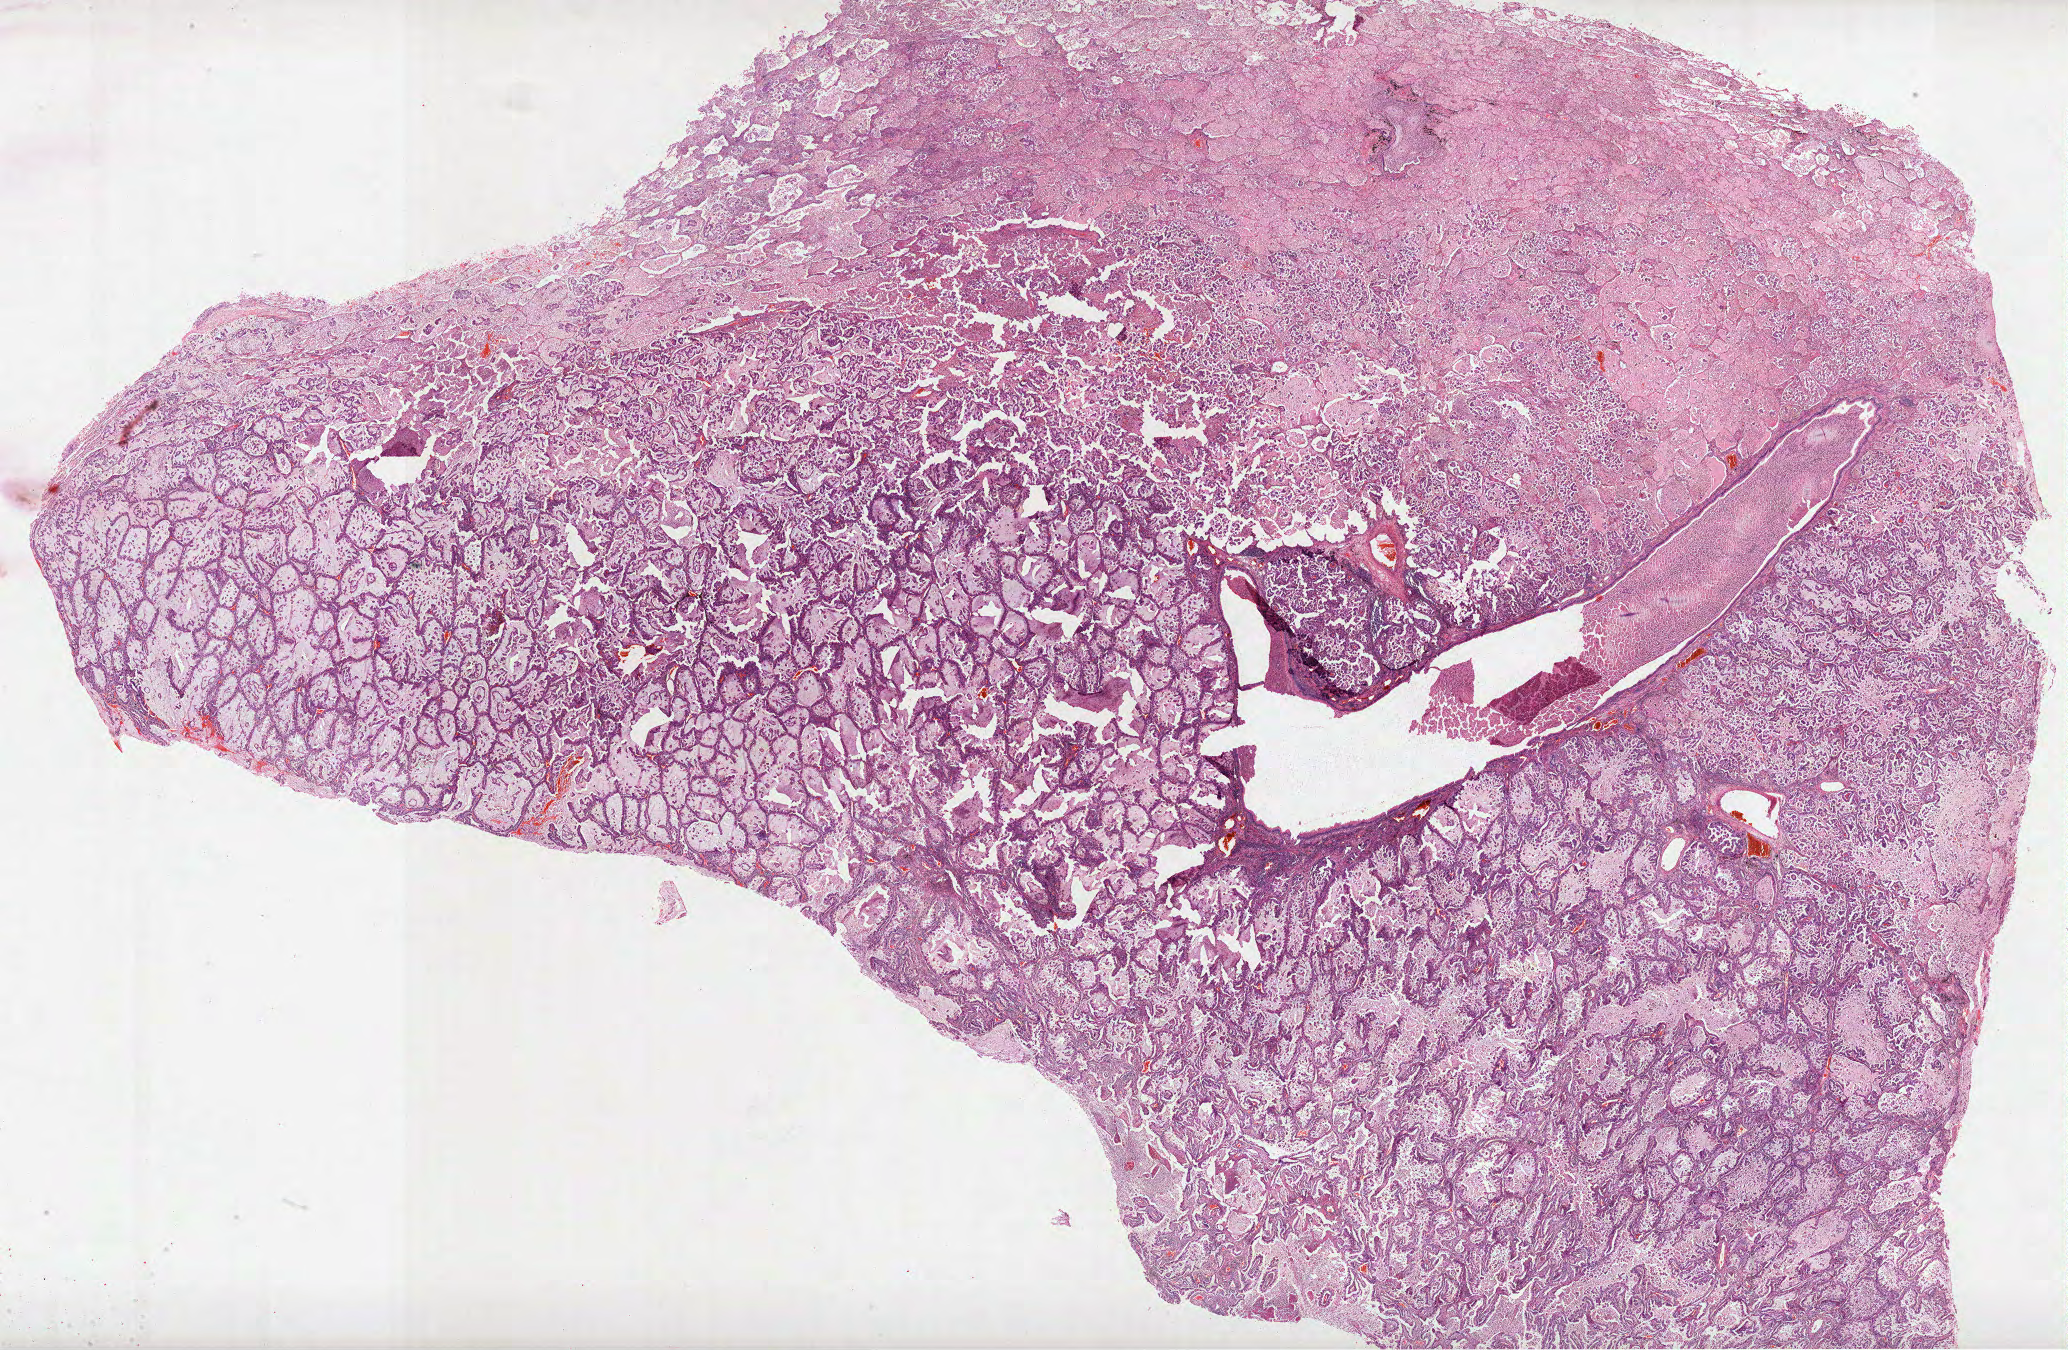
Hematoxylin and eosin (H&E) stained whole-slide image — whole scanned area (about 33.4 x 21.8 mm, slide scanned at 40x) shown as a low-resolution overview. Formalin-fixed paraffin-embedded (FFPE) diagnostic section. Primary tumour sample from the lung. Male, age 52 years at initial diagnosis.
- diagnosis: Adenocarcinoma, NOS (lower lobe, lung)
- AJCC pathologic stage: IIIA